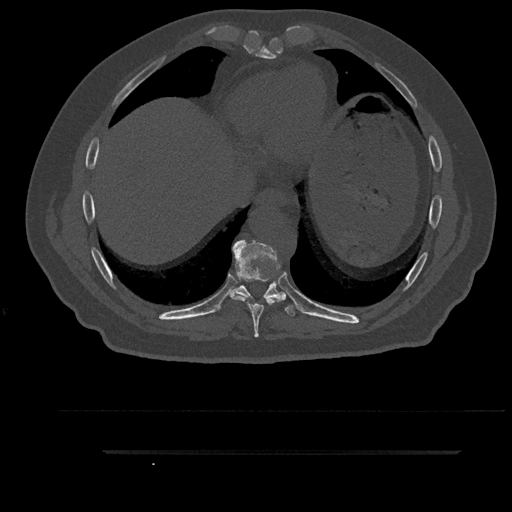
CT including the spine, one axial slice. Slice 450 of 797 in the series (ordered by position). Reconstruction kernel Br40s/3. 120 kVp. Bone window (W 1800 / L 400 HU). 0.5 mm slice thickness. 512 × 512 image matrix, field of view 432 × 432 mm. Male patient, age 63 years. Case-level facts recorded for this patient, not image findings: primary cancer: renal.
Outlined on this slice (semi-automatically segmented with operator editing):
- T8 vertebra: bounding box (x1, y1, x2, y2) in pixels: (230, 239, 286, 338)
- T9 vertebra: (216, 253, 295, 316)